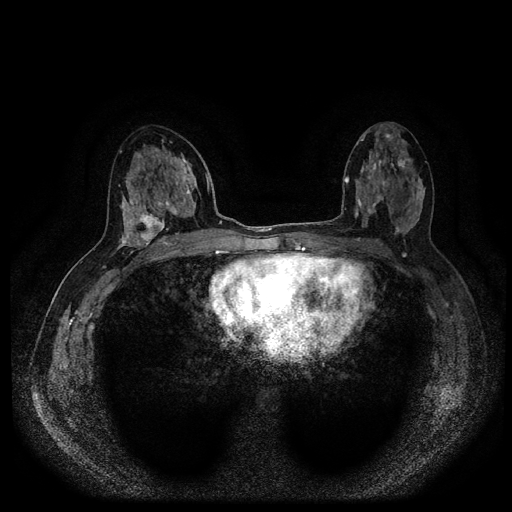
Breast MRI (dynamic contrast-enhanced, multi-phase), one axial slice; slice 51 of 116 in the series (ordered by position); dynamic contrast-enhanced series, time point 2 of 5 at this slice position (early post-contrast); 1.5 T; TE 2.6 ms, TR 5.4 ms; 512 × 512 image matrix, field of view 340 × 340 mm. Female patient, age 48 years.
Outlined on this slice (semi-automatically segmented with operator editing):
- breast lesion (labelled 'tumour' in the annotation; benign lesions carry a separate 'benign' label): bounding box (x1, y1, x2, y2) in pixels: (136, 207, 165, 247)